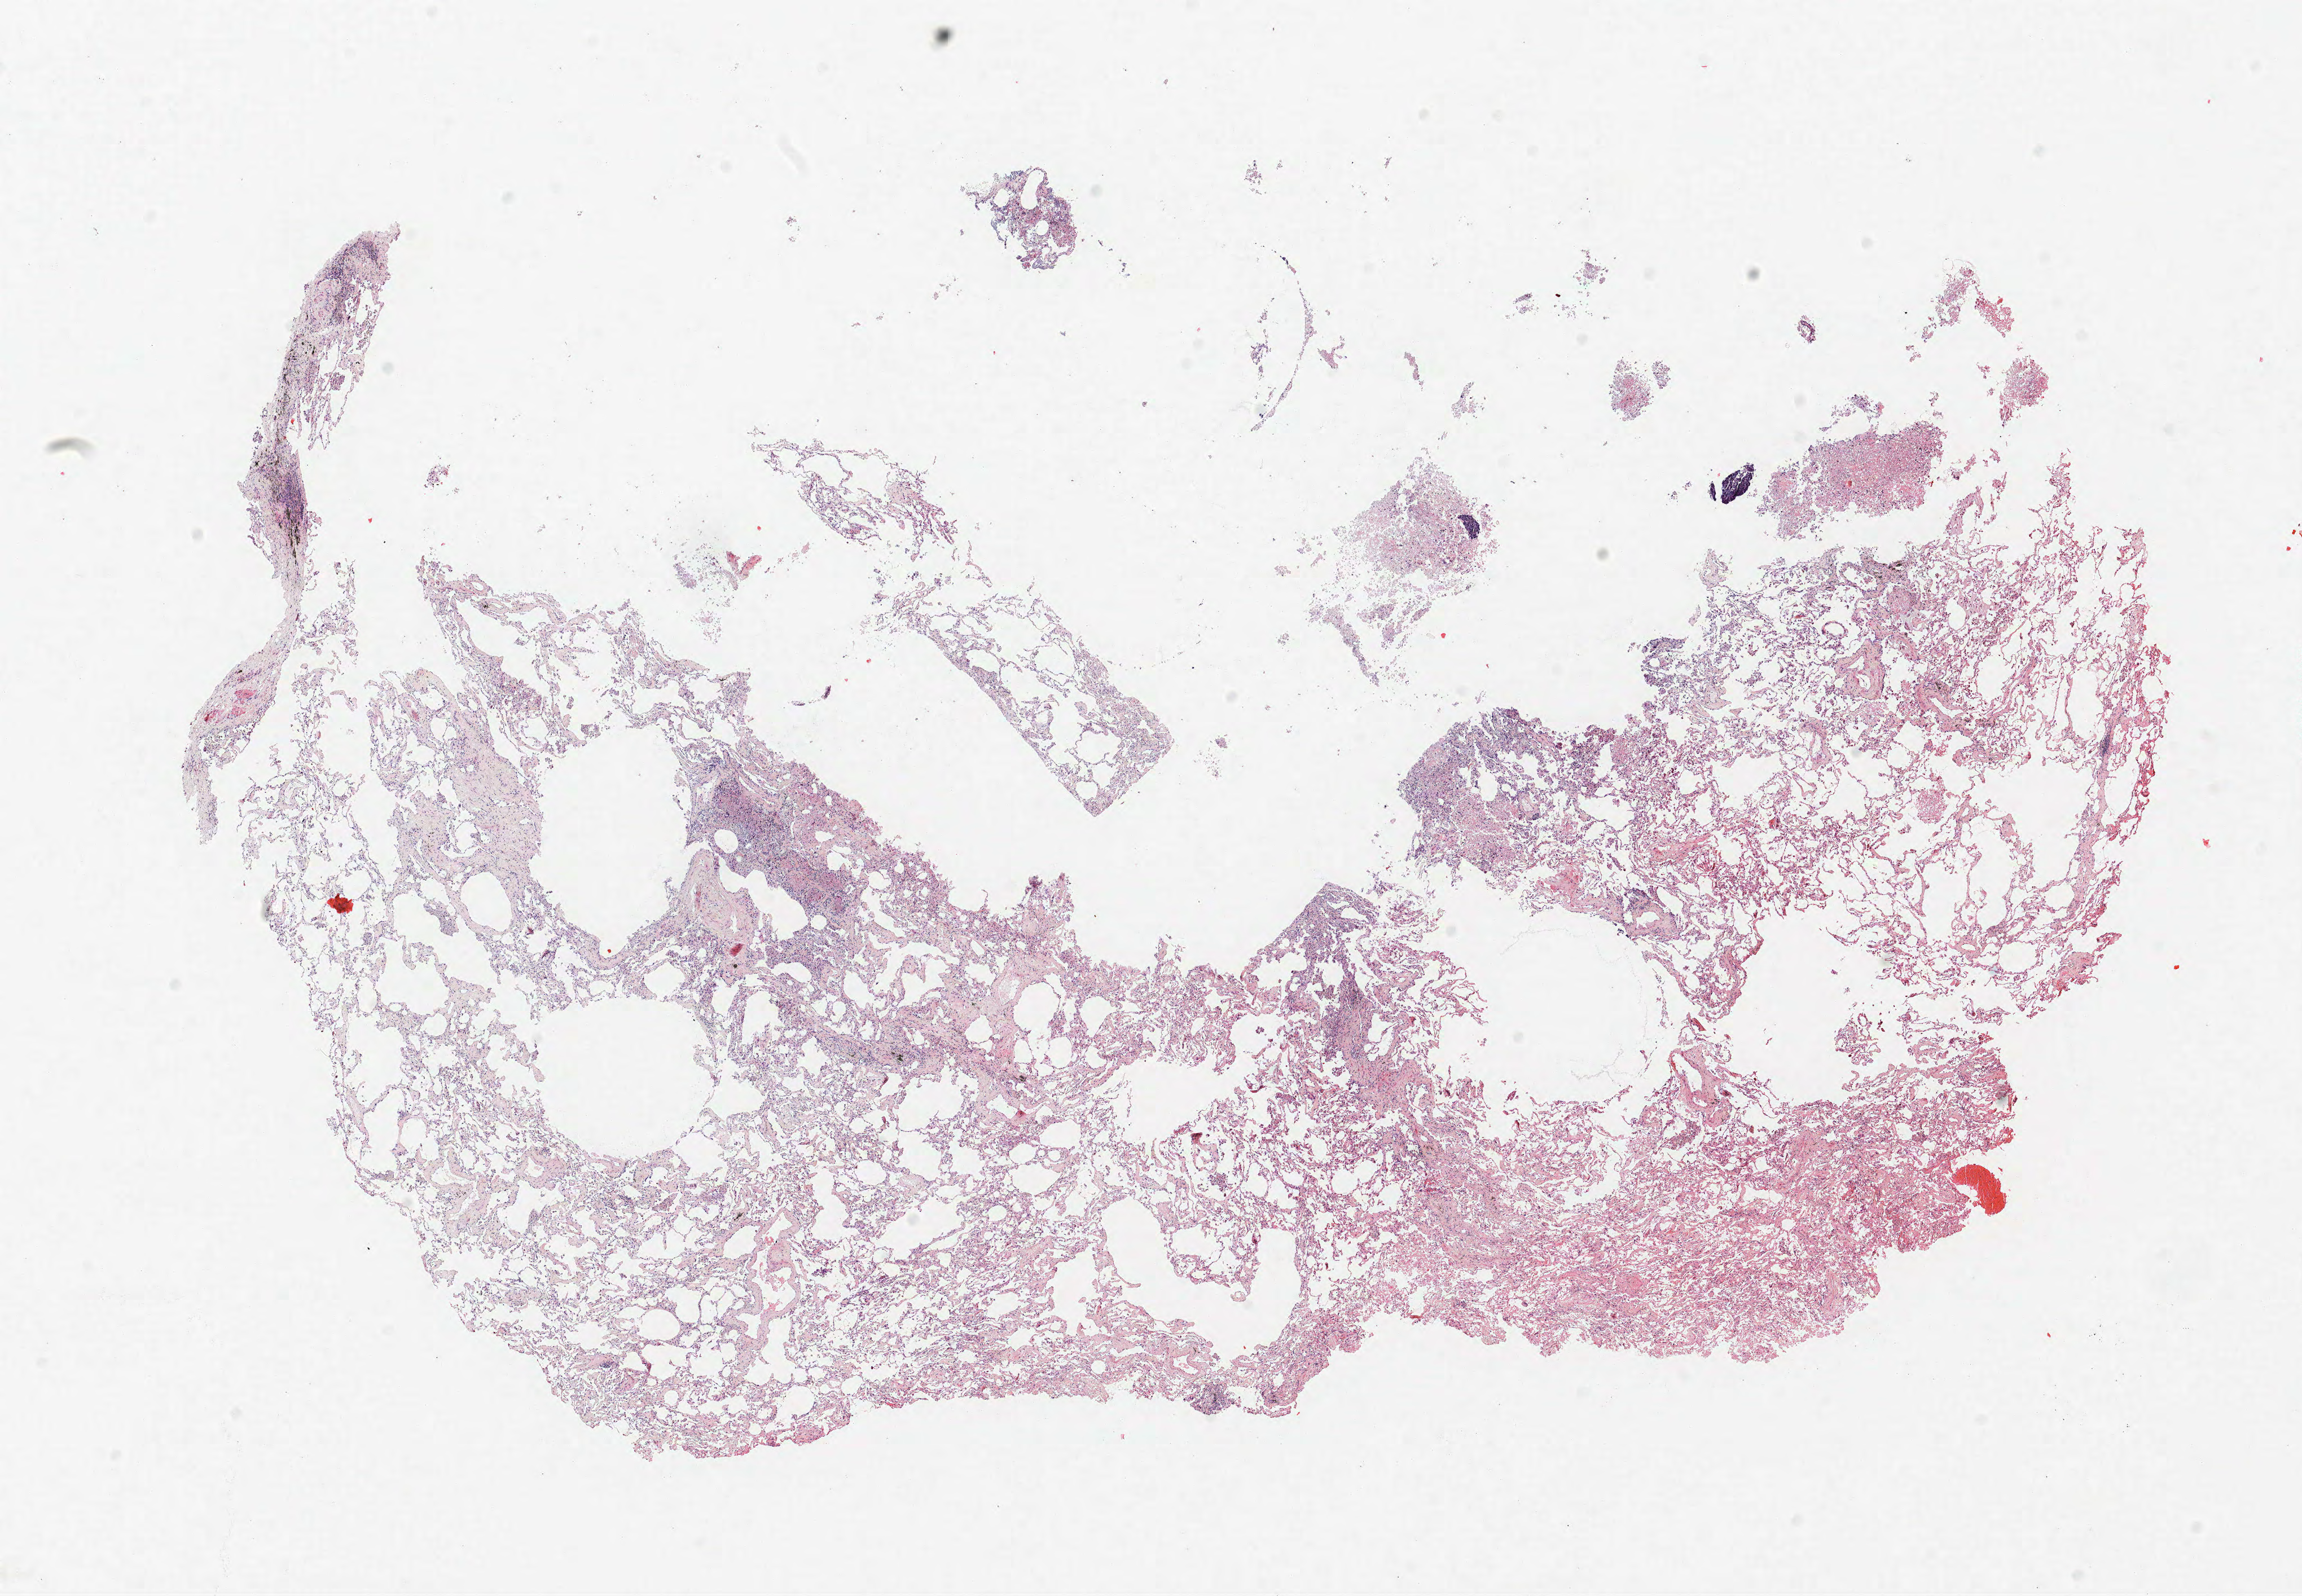
Hematoxylin and eosin (H&E) stained whole-slide image — whole scanned area (about 16.3 x 11.3 mm, slide scanned at 40x) shown as a low-resolution overview, FFPE section, lung. Male, age 61 at enrolment. Grade: poorly differentiated (G3).
Participant's lung-cancer diagnosis: Squamous cell carcinoma, NOS. Tumour size (pathology): 12 mm. Primary tumour location (clinical record): right upper lobe. Stage (AJCC 6th edition): IIIB.